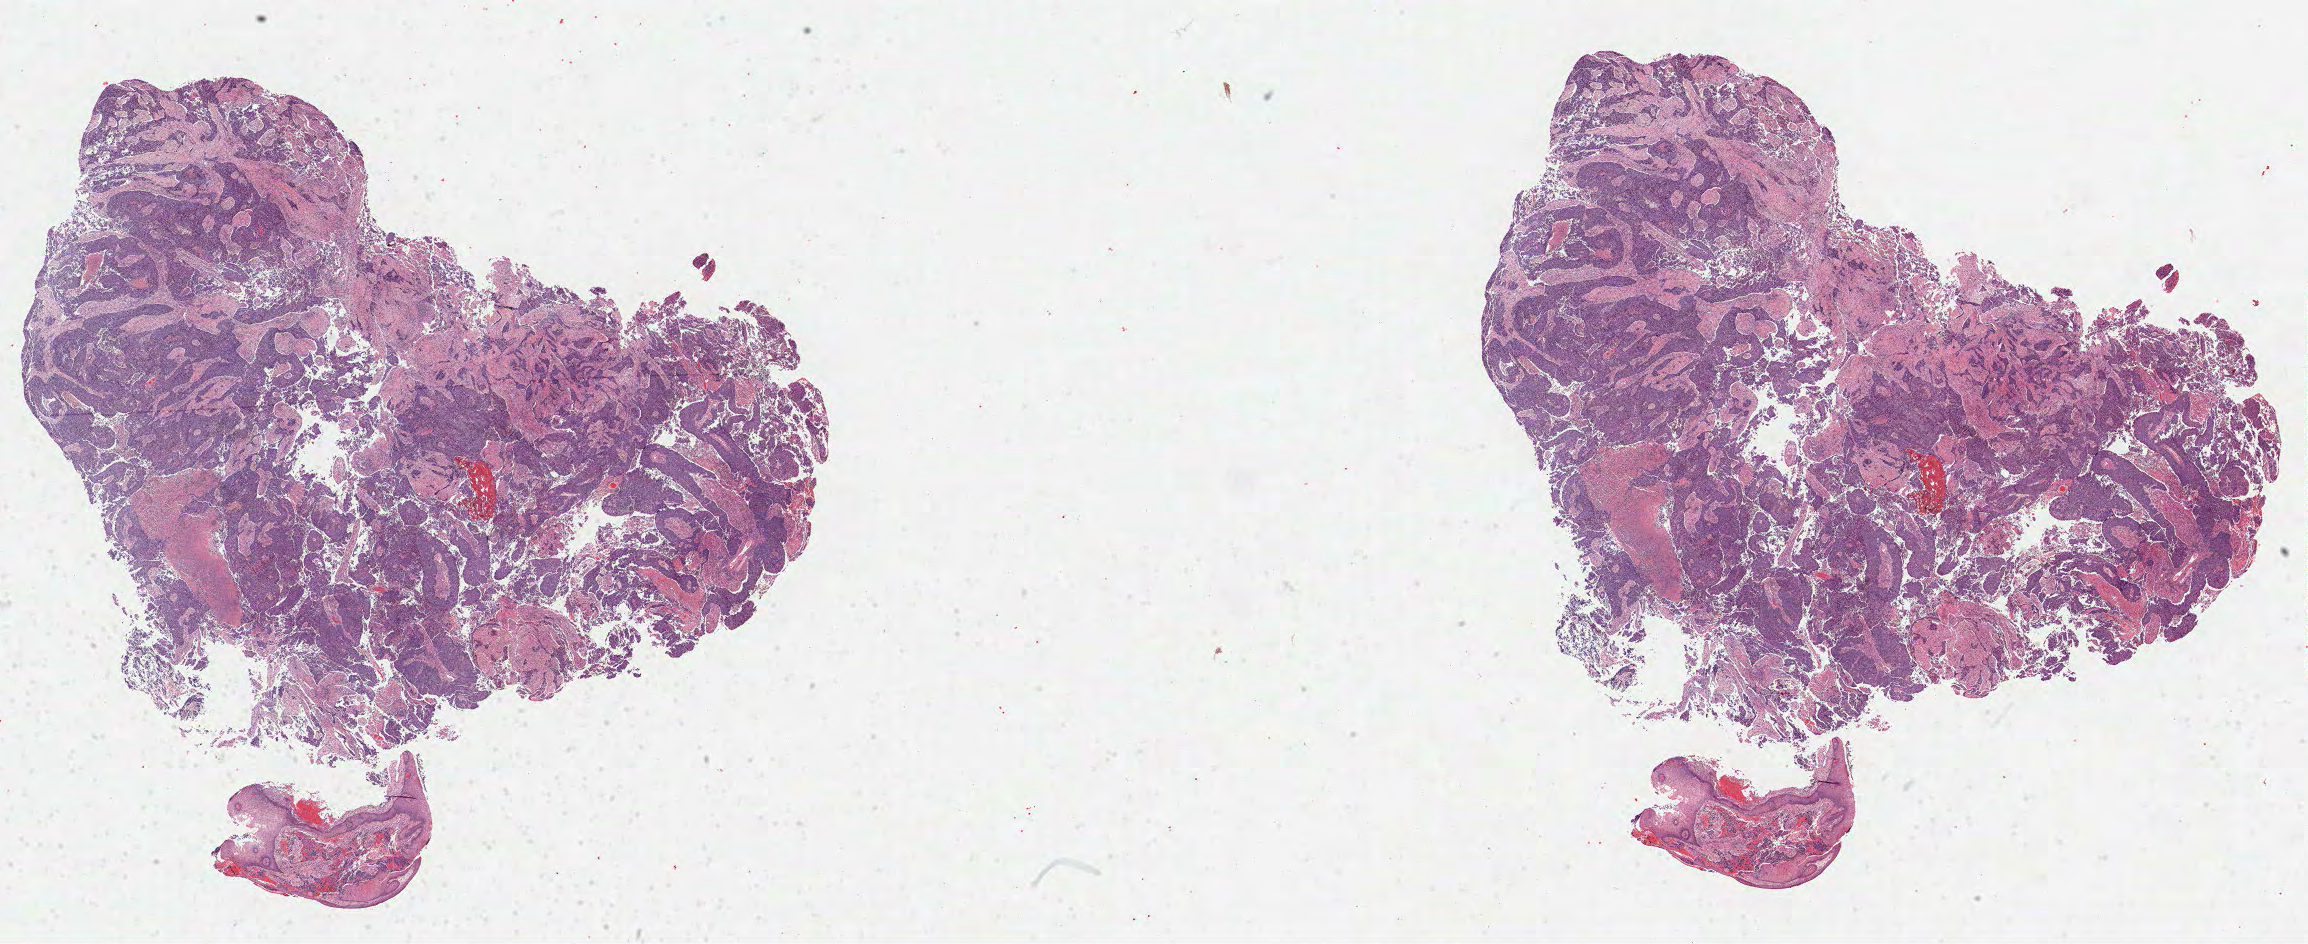
Digitized H&E-stained tissue section (whole slide), low-resolution overview of the scanned area, about 37.2 x 15.2 mm; FFPE section; head and neck, primary tumour sample. Patient: male, age at initial diagnosis 75 years. Histologic grade: G2 (moderately differentiated).
• laterality: left
• pathologic diagnosis: Squamous cell carcinoma, NOS (base of tongue, NOS)